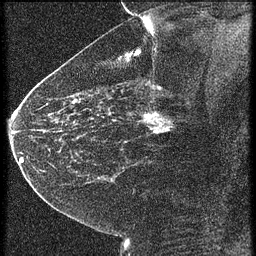
Breast MRI (dynamic contrast-enhanced), one sagittal slice; slice 37 of 60 in the series (ordered by position); 4 images stored at this slice position (order not interpretable as contrast timing); 1.5 T; TE 4.2 ms, TR 21.3 ms; 1.5 mm slice thickness; 256 × 256 image matrix. Patient: female, 43 years. From the clinical record (not read from this slice): setting: breast cancer imaged before/during neoadjuvant chemotherapy; receptor status: HER2-positive.
Annotated regions visible in this slice (semi-automatic segmentation, software-assisted and operator-edited):
- analysis volume of interest (the breast-tissue region the enhancement analysis was run in; not a lesion): bounding box <122,100,187,151> (left, top, right, bottom; pixels)
- tumour enhancement mask (voxels above the 90 % enhancement threshold inside the analysis volume of interest): <144,112,173,133>